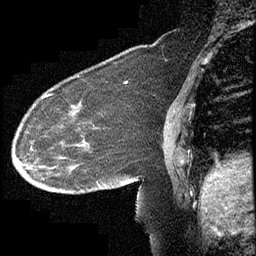
Breast MRI (dynamic contrast-enhanced), one sagittal slice. Slice 152 of 232 in the series (ordered by position). Dynamic contrast-enhanced study with each time point stored as its own series, time point 2 of 4 at this slice position (early post-contrast, ordered by acquisition time). 1.5 T. TE 4.2 ms, TR 6.7 ms. 256 × 256 image matrix. Patient: female, 63 years. From the clinical record (not read from this slice): setting: breast cancer imaged before/during neoadjuvant chemotherapy; receptor status: triple-negative.
Outlined on this slice (semi-automatic segmentation, software-assisted and operator-edited):
- analysis volume of interest (the breast-tissue region the enhancement analysis was run in; not a lesion): bounding box [x1, y1, x2, y2] px = [13, 90, 140, 211]
- tumour enhancement mask (voxels above the 70 % enhancement threshold inside the analysis volume of interest): [47, 94, 51, 96]